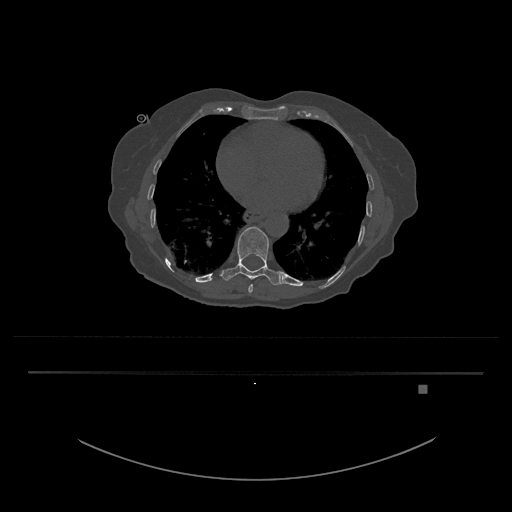
CT including the spine, one axial slice. Position 719 of 797 along the scan axis. Reconstruction kernel Br40s/3. Bone window (W 1800 / L 400 HU). 512 × 512 image matrix, field of view 500 × 500 mm. Patient: female, 57 years. From the clinical record (not read from this slice): primary cancer: cervical.
Annotated regions visible in this slice (semi-automatically segmented with operator editing):
- T10 vertebra: bounding box (x1, y1, x2, y2) in pixels: (221, 226, 285, 285)
- T9 vertebra: (248, 284, 253, 293)